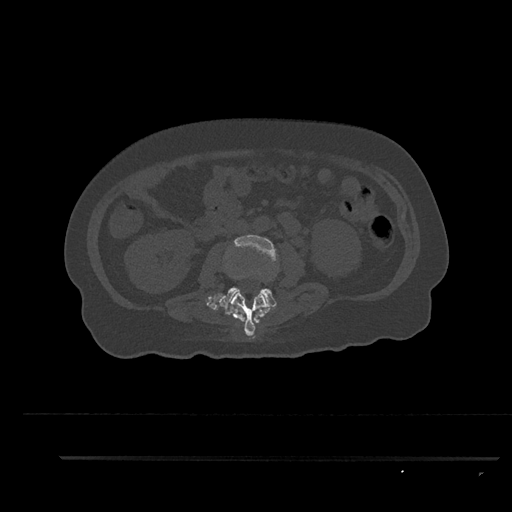
CT including the spine, one axial slice; slice 121 of 797 in the series (ordered by position); 120 kVp; bone window (W 1800 / L 400 HU); 512 × 512 image matrix, field of view 408 × 408 mm. Patient: female, 44 years. Case-level facts recorded for this patient, not image findings: primary cancer: renal; vertebrae with lytic lesions (as recorded): L1.
Structures marked on this image (semi-automatic segmentation, software-assisted and operator-edited):
- L2 vertebra: bounding box (x1, y1, x2, y2) in pixels: (225, 292, 269, 336)
- L3 vertebra: (220, 235, 279, 308)